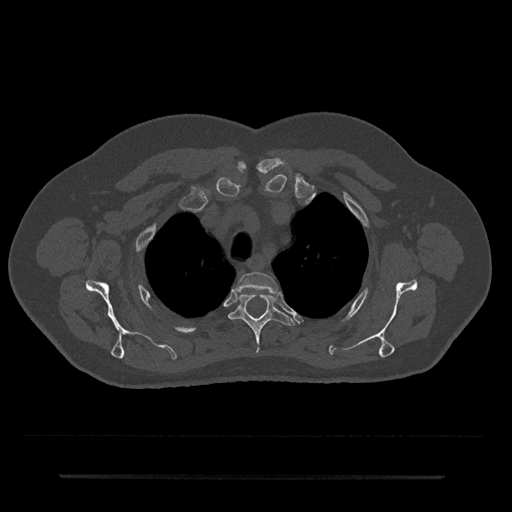
CT including the spine, one axial slice. Position 574 of 797 along the scan axis. 120 kVp. Bone window (W 1800 / L 400 HU). 0.5 mm slice thickness. 512 × 512 image matrix, field of view 437 × 437 mm. Patient: male, 69 years. From the clinical record (not read from this slice): primary cancer: prostate.
Annotated regions visible in this slice (semi-automatically segmented with operator editing):
- T2 vertebra: bounding box [x1, y1, x2, y2] px = [236, 272, 278, 294]
- T3 vertebra: [229, 293, 295, 354]